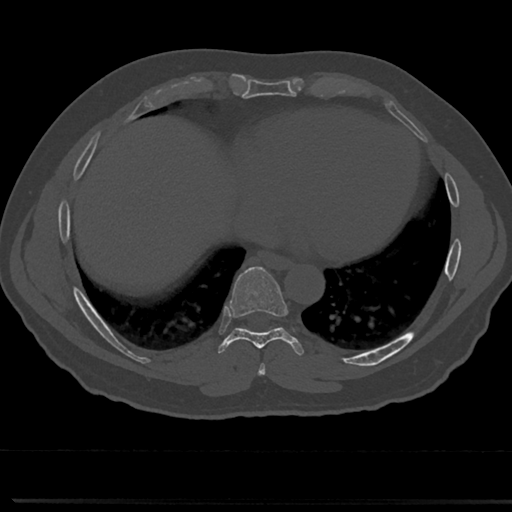
CT including the spine, one axial slice; position 350 of 817 along the scan axis; 120 kVp; bone window (W 1800 / L 400 HU); 0.5 mm slice thickness; 512 × 512 image matrix, field of view 355 × 355 mm. Male patient, age 61 years. From the clinical record (not read from this slice): primary cancer: prostate.
Outlined on this slice (semi-automatically segmented with operator editing):
- T7 vertebra: box from (x=254, y=340) to (x=271, y=376) px
- T8 vertebra: (x=219, y=271)–(x=301, y=350)